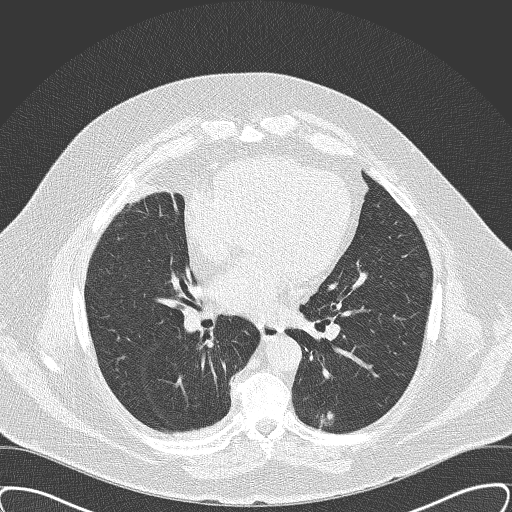
Axial slice from a low-dose chest CT screening exam. Third annual screen. Lung window (W 1500 / L -600 HU). Slice 86 of 161 in the series. 512 × 512 image matrix. Male, age 63 years at enrolment. Former smoker at enrolment.
Expert-annotated lung lesion, bounding box (x1, y1, x2, y2) in pixels: (300, 393, 354, 448). The screening reader recorded 2 non-calcified nodules or masses ≥4 mm on this exam; which of them this box marks is not recorded. Participant outcome: lung cancer diagnosed 47 days after this screen — squamous cell carcinoma, NOS, left lower lobe, moderately differentiated (G2), stage IA (AJCC 6th edition), 15 mm at pathology.